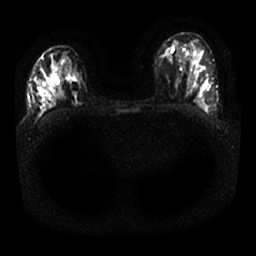
Breast MRI, one axial slice. Slice 13 of 25 in the series (ordered by position). Diffusion-weighted series; image 2 of 4 stored at this slice position (different b-values; order by instance number). 1.5 T. 4 mm slice thickness. 256 × 256 image matrix, field of view 330 × 330 mm. Female patient.
Annotated regions visible in this slice (outlined manually by an expert reader):
- tumour on diffusion-weighted imaging: bounding box [x1, y1, x2, y2] px = [69, 86, 77, 97]